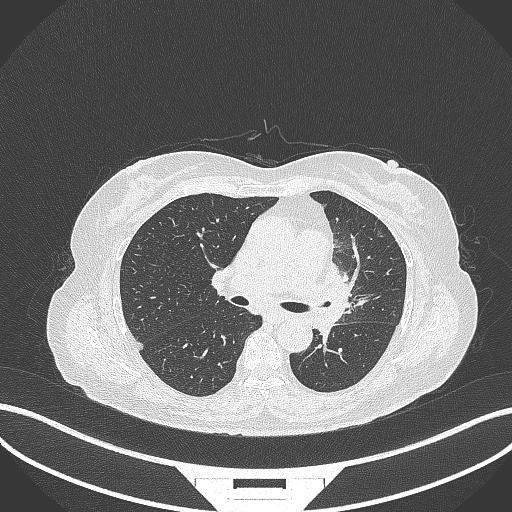
Chest CT, one axial slice. Slice 196 of 382 in the series (ordered by position). Lung window (W 1500 / L -600 HU). 1 mm slice thickness. 512 × 512 image matrix, field of view 400 × 400 mm. Patient: female, 64 years. From the clinical record (not read from this slice): clinical TNM (as recorded): T2a N2 M0.
Outlined on this slice (bounding box drawn by a radiologist):
- lung tumour (recorded histology: adenocarcinoma): bounding box [x1, y1, x2, y2] px = [321, 255, 362, 335]